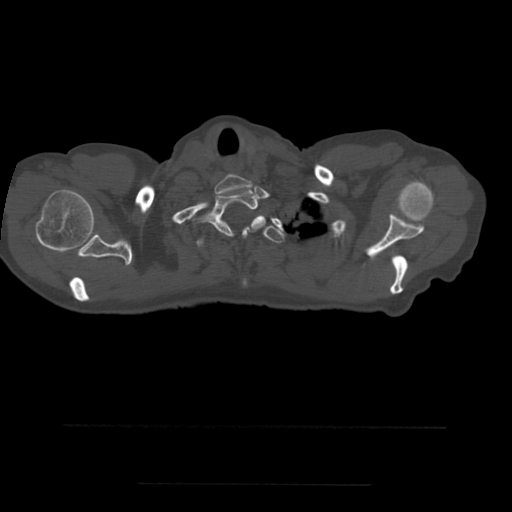
CT including the spine, one axial slice; slice 443 of 544 in the series (ordered by position); bone window (W 1800 / L 400 HU); 512 × 512 image matrix. Patient age 58 years. Case-level facts recorded for this patient, not image findings: primary cancer: lung.
Structures marked on this image (semi-automatic segmentation, software-assisted and operator-edited):
- T1 vertebra: bounding box (x1, y1, x2, y2) in pixels: (192, 188, 259, 237)
- T2 vertebra: (197, 215, 285, 285)